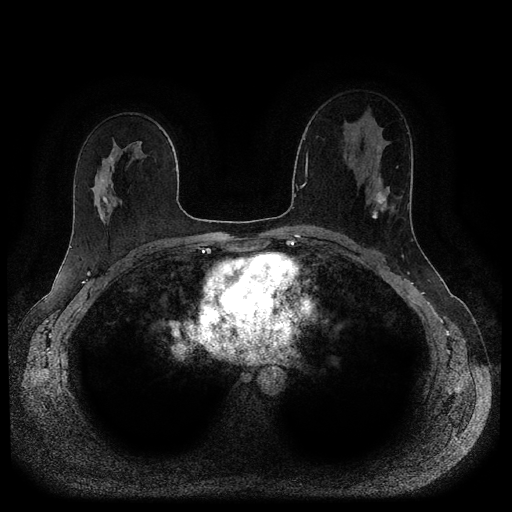
Breast MRI (dynamic contrast-enhanced, multi-phase), one axial slice; slice 59 of 116 in the series (ordered by position); dynamic contrast-enhanced series, time point 2 of 5 at this slice position (early post-contrast); 1.5 T; TE 2.6 ms, TR 5.3 ms; 2 mm slice thickness; 512 × 512 image matrix, field of view 350 × 350 mm. Female patient, age 45 years.
Annotated regions visible in this slice (semi-automatic segmentation, software-assisted and operator-edited):
- breast lesion (labelled 'tumour' in the annotation; benign lesions carry a separate 'benign' label): box from (x=373, y=192) to (x=387, y=209) px